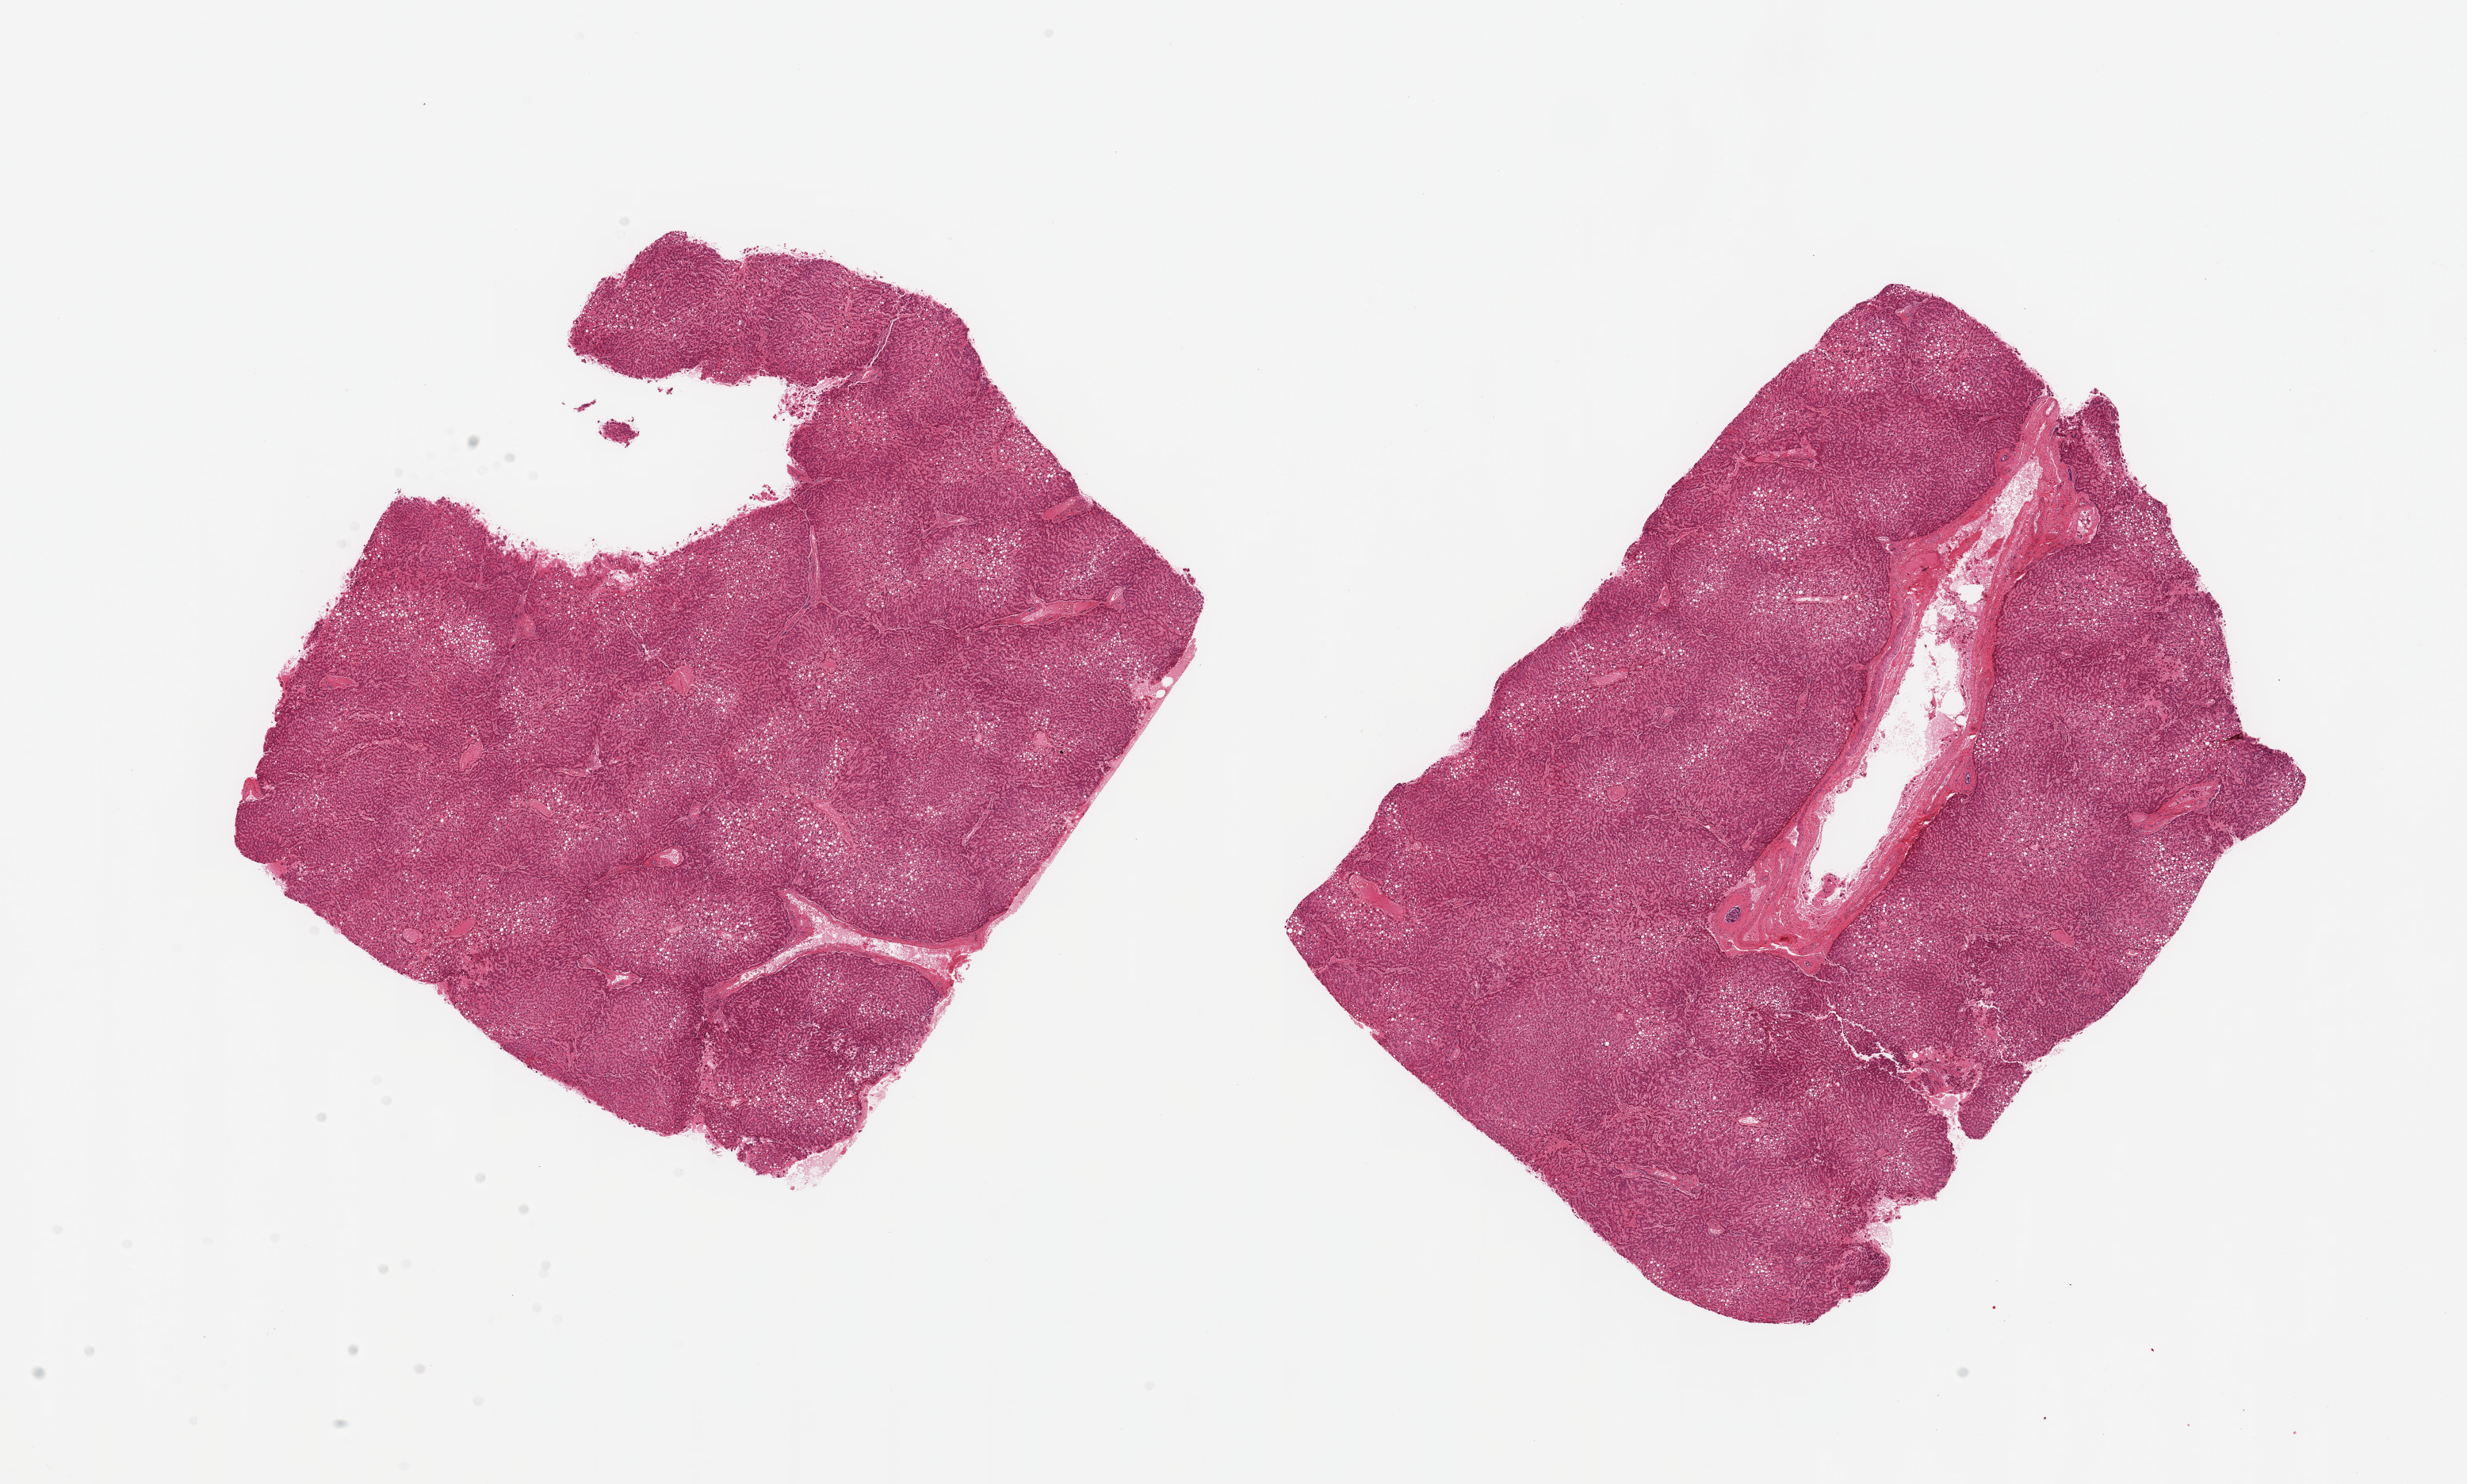
Haematoxylin and eosin whole-slide image — a low-resolution overview of the entire scanned area, about 24.6 x 14.8 mm (from a 20x scan). PAXgene-fixed, paraffin-embedded tissue. Target tissue: liver. Donor tissue sample. Male donor.
- reviewer comment on this tissue sample: 2 pieces; moderate macrovesicular steatosis